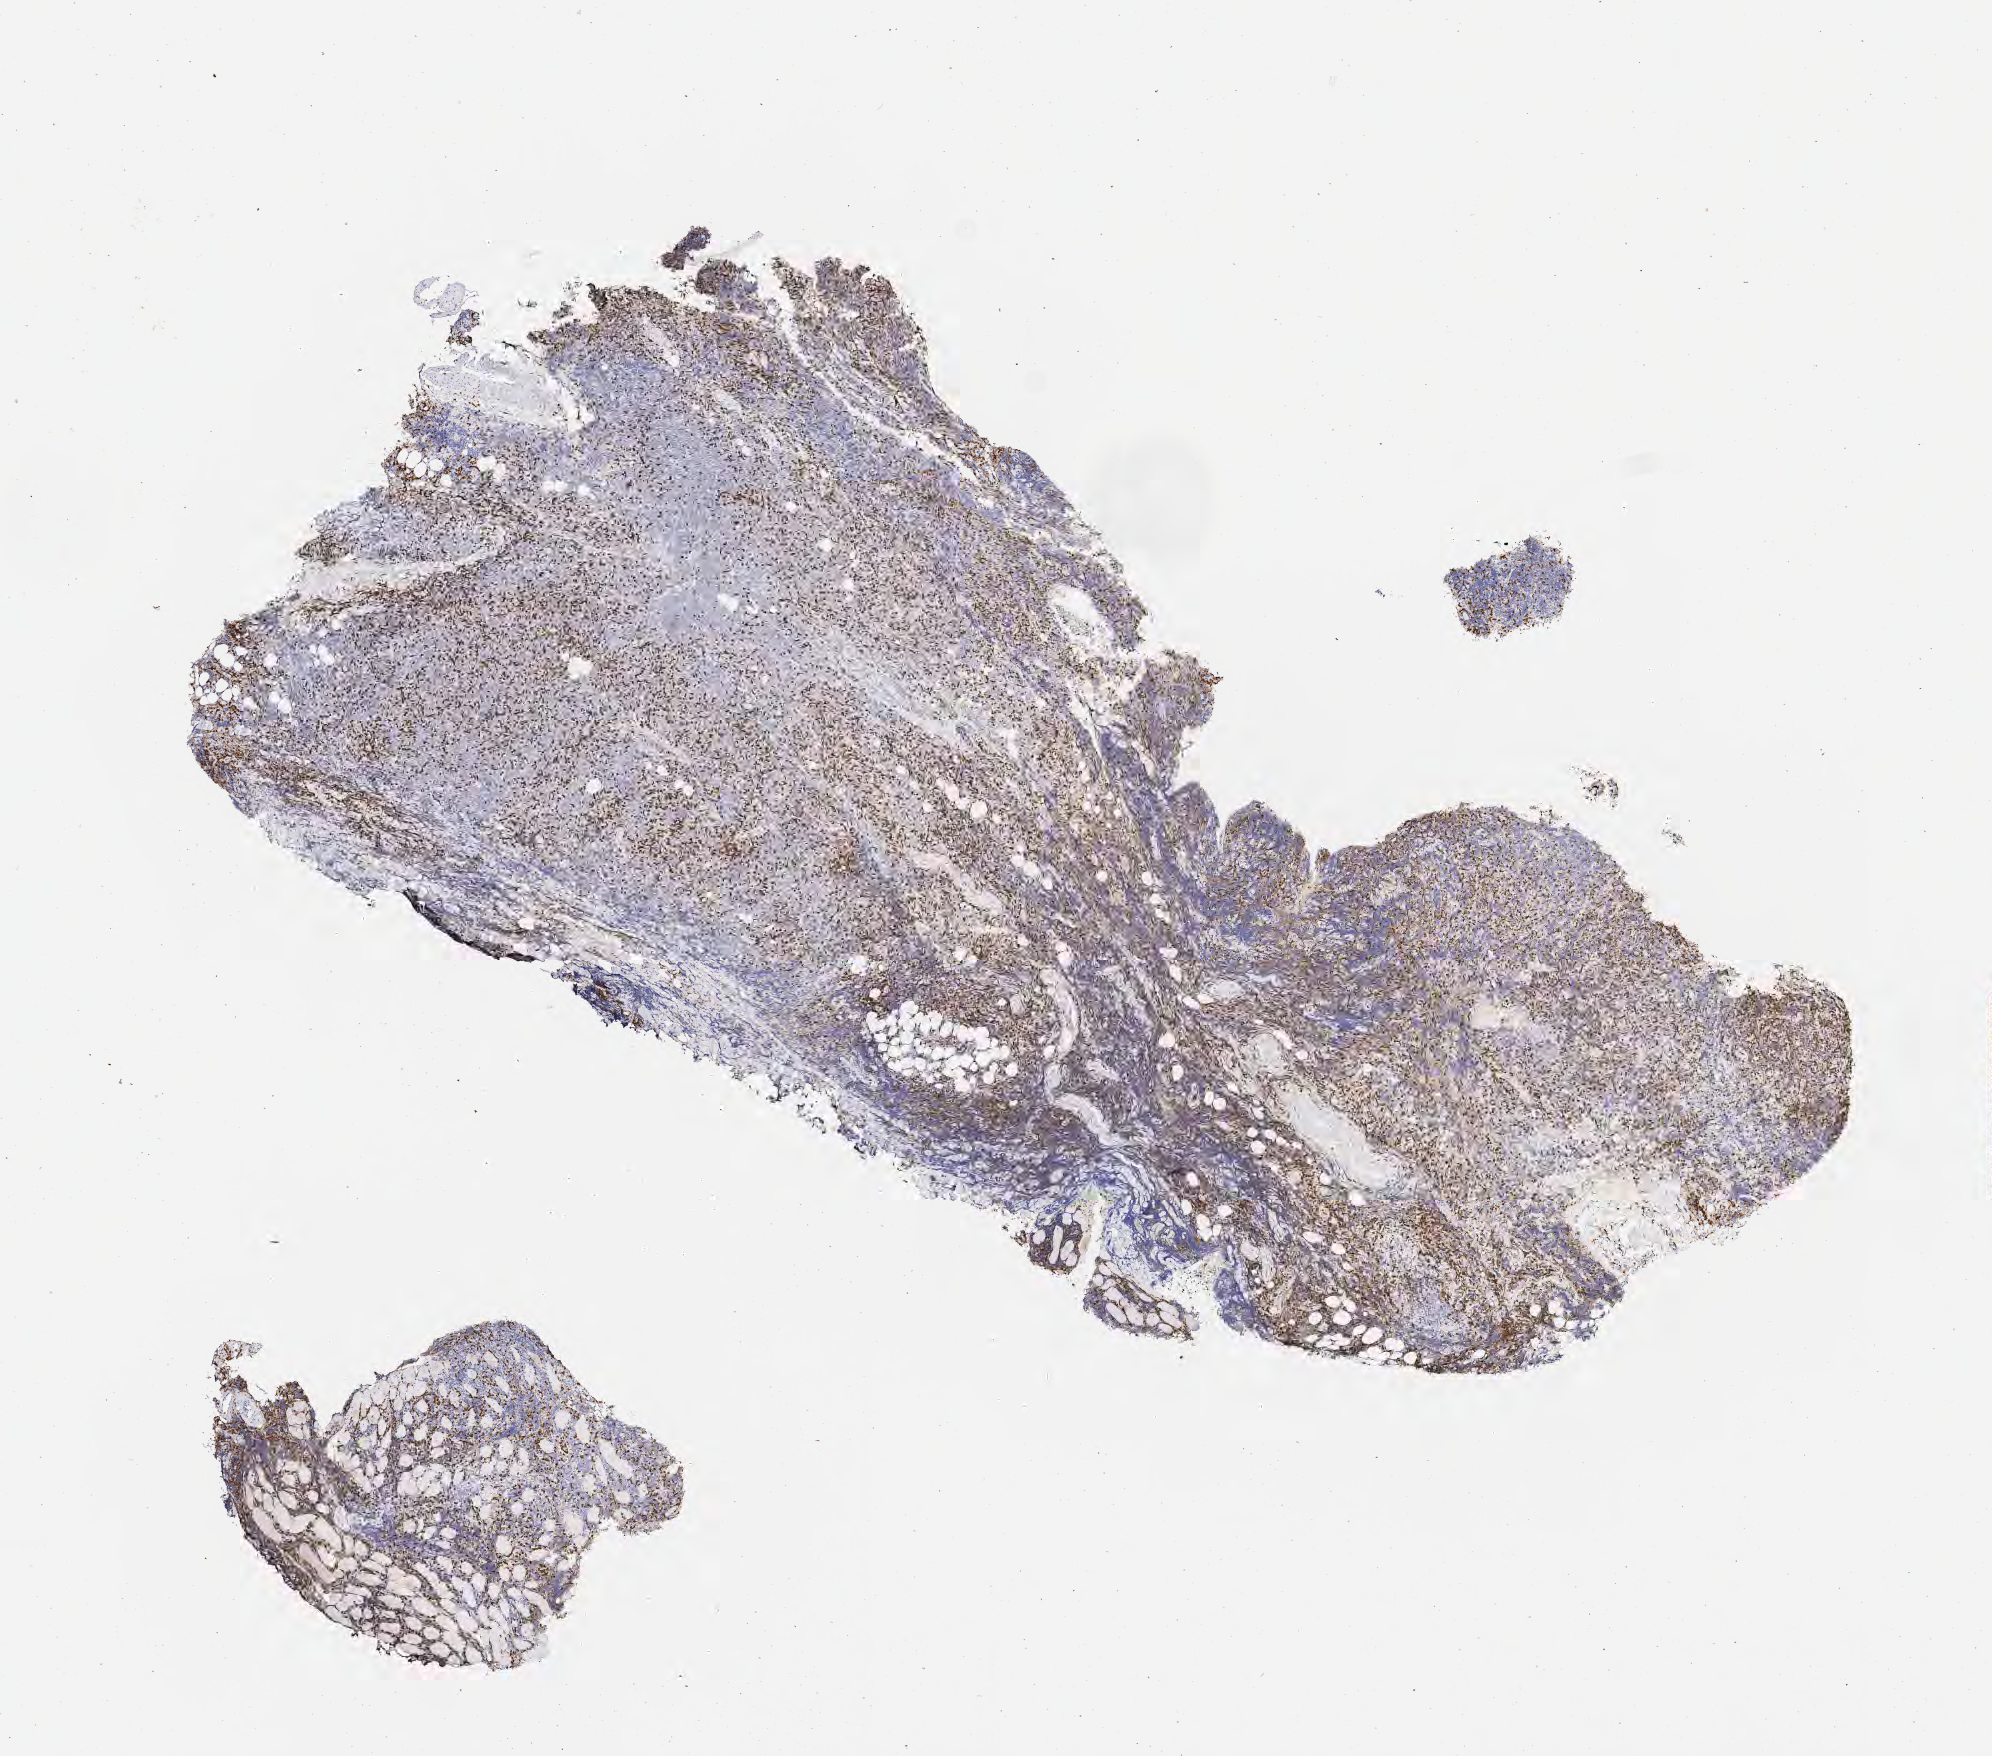
IHC for CD3, whole-slide image, shown as a low-resolution overview of the whole scanned area (about 8.0 x 7.1 mm); tumor tissue. Male patient, age 67 years.
Diagnosis: Diffuse large B-cell lymphoma, NOS.